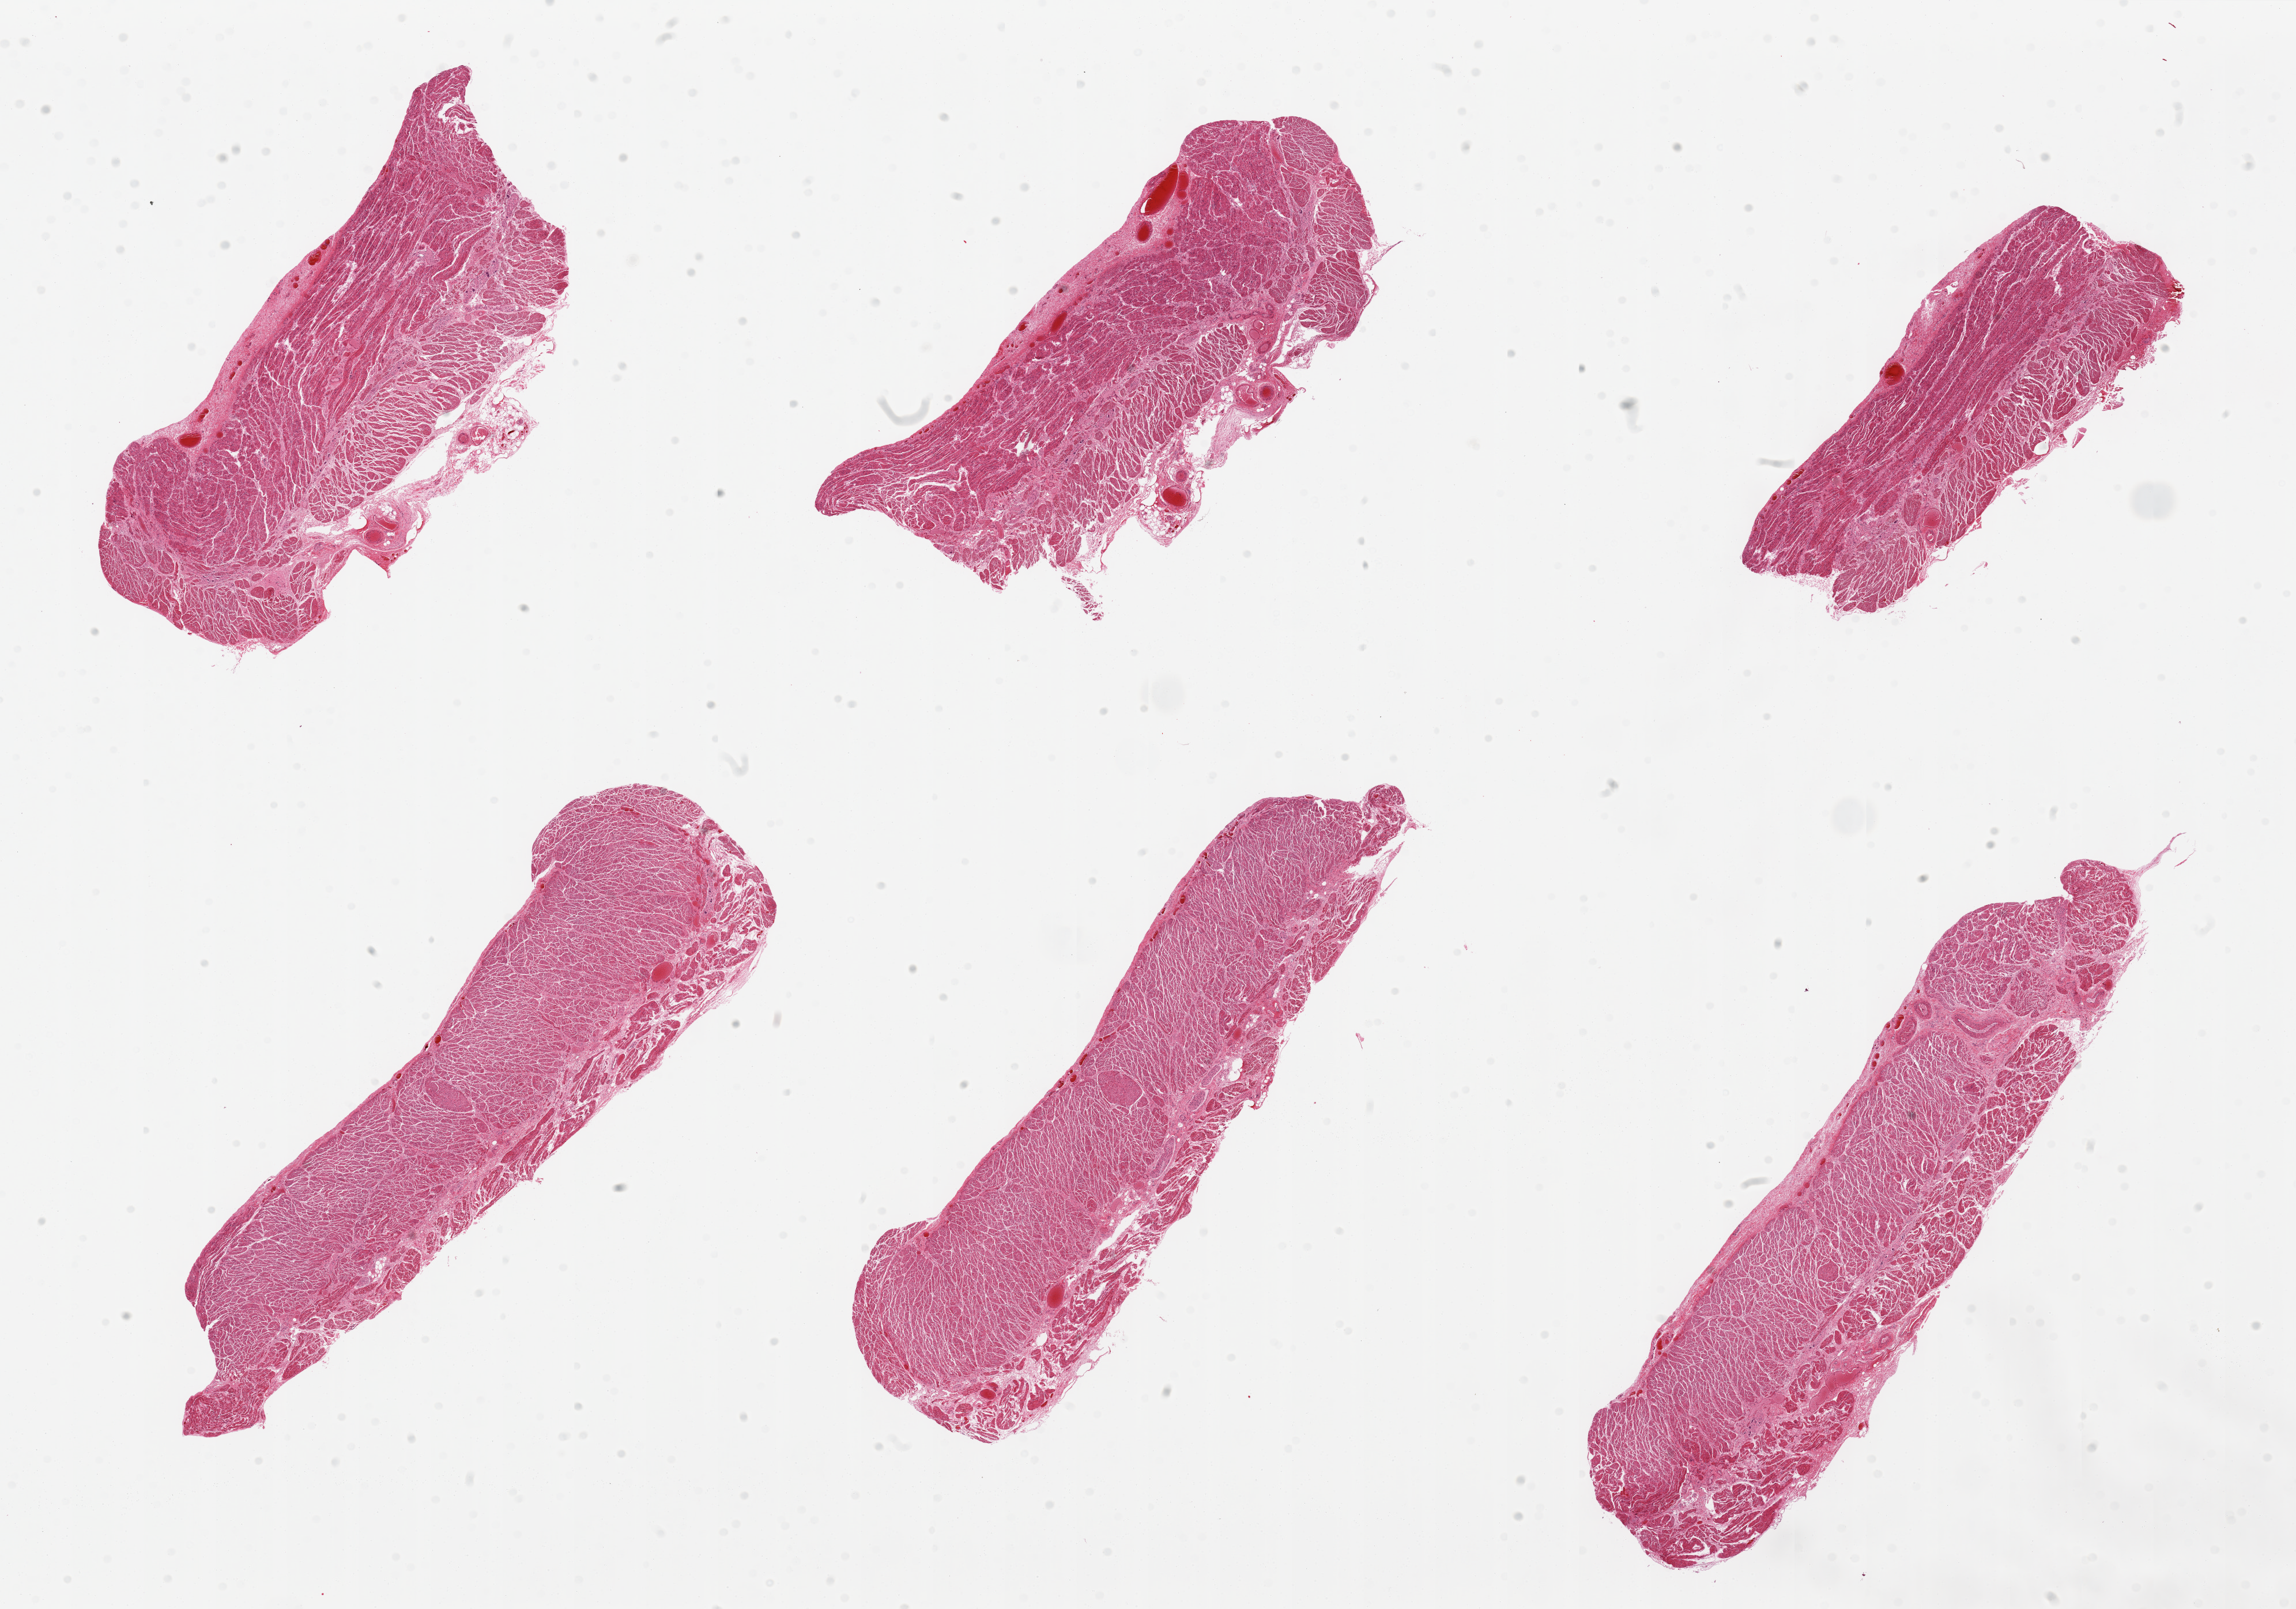
Digitized H&E-stained section — low-resolution overview of the scanned area, about 31.5 x 22.1 mm (from a 20x scan), PAXgene-fixed paraffin-embedded (PFPE) section, section of esophageal muscle (target tissue), donor tissue sample.
• reviewer comment on this tissue sample: 6 pieces, well trimmed muscle